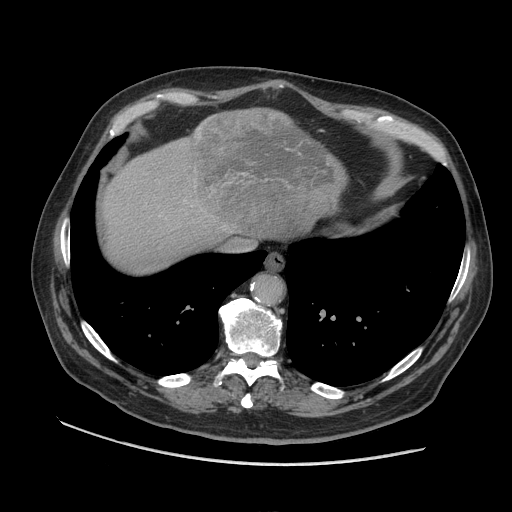
Contrast-enhanced abdominal CT (liver protocol), one axial slice. Slice 87 of 109 in the series (ordered by position). Reconstruction kernel STANDARD. Soft-tissue window (W 400 / L 40 HU). 2.5 mm slice thickness. 512 × 512 image matrix, field of view 420 × 420 mm. From the clinical record (not read from this slice): diagnosis: hepatocellular carcinoma (patient treated with transarterial chemoembolisation; whether this scan precedes or follows treatment is not stated here); TNM stage (as recorded): Stage-I; Child-Pugh class: A; tumour nodularity: uninodular.
Outlined on this slice (semi-automatically segmented with operator editing):
- liver parenchyma outside the tumour (the mass and vessels are separate outlines, so this box may not span the whole liver): bounding box [x1, y1, x2, y2] px = [102, 112, 340, 272]
- mass: [189, 107, 347, 235]